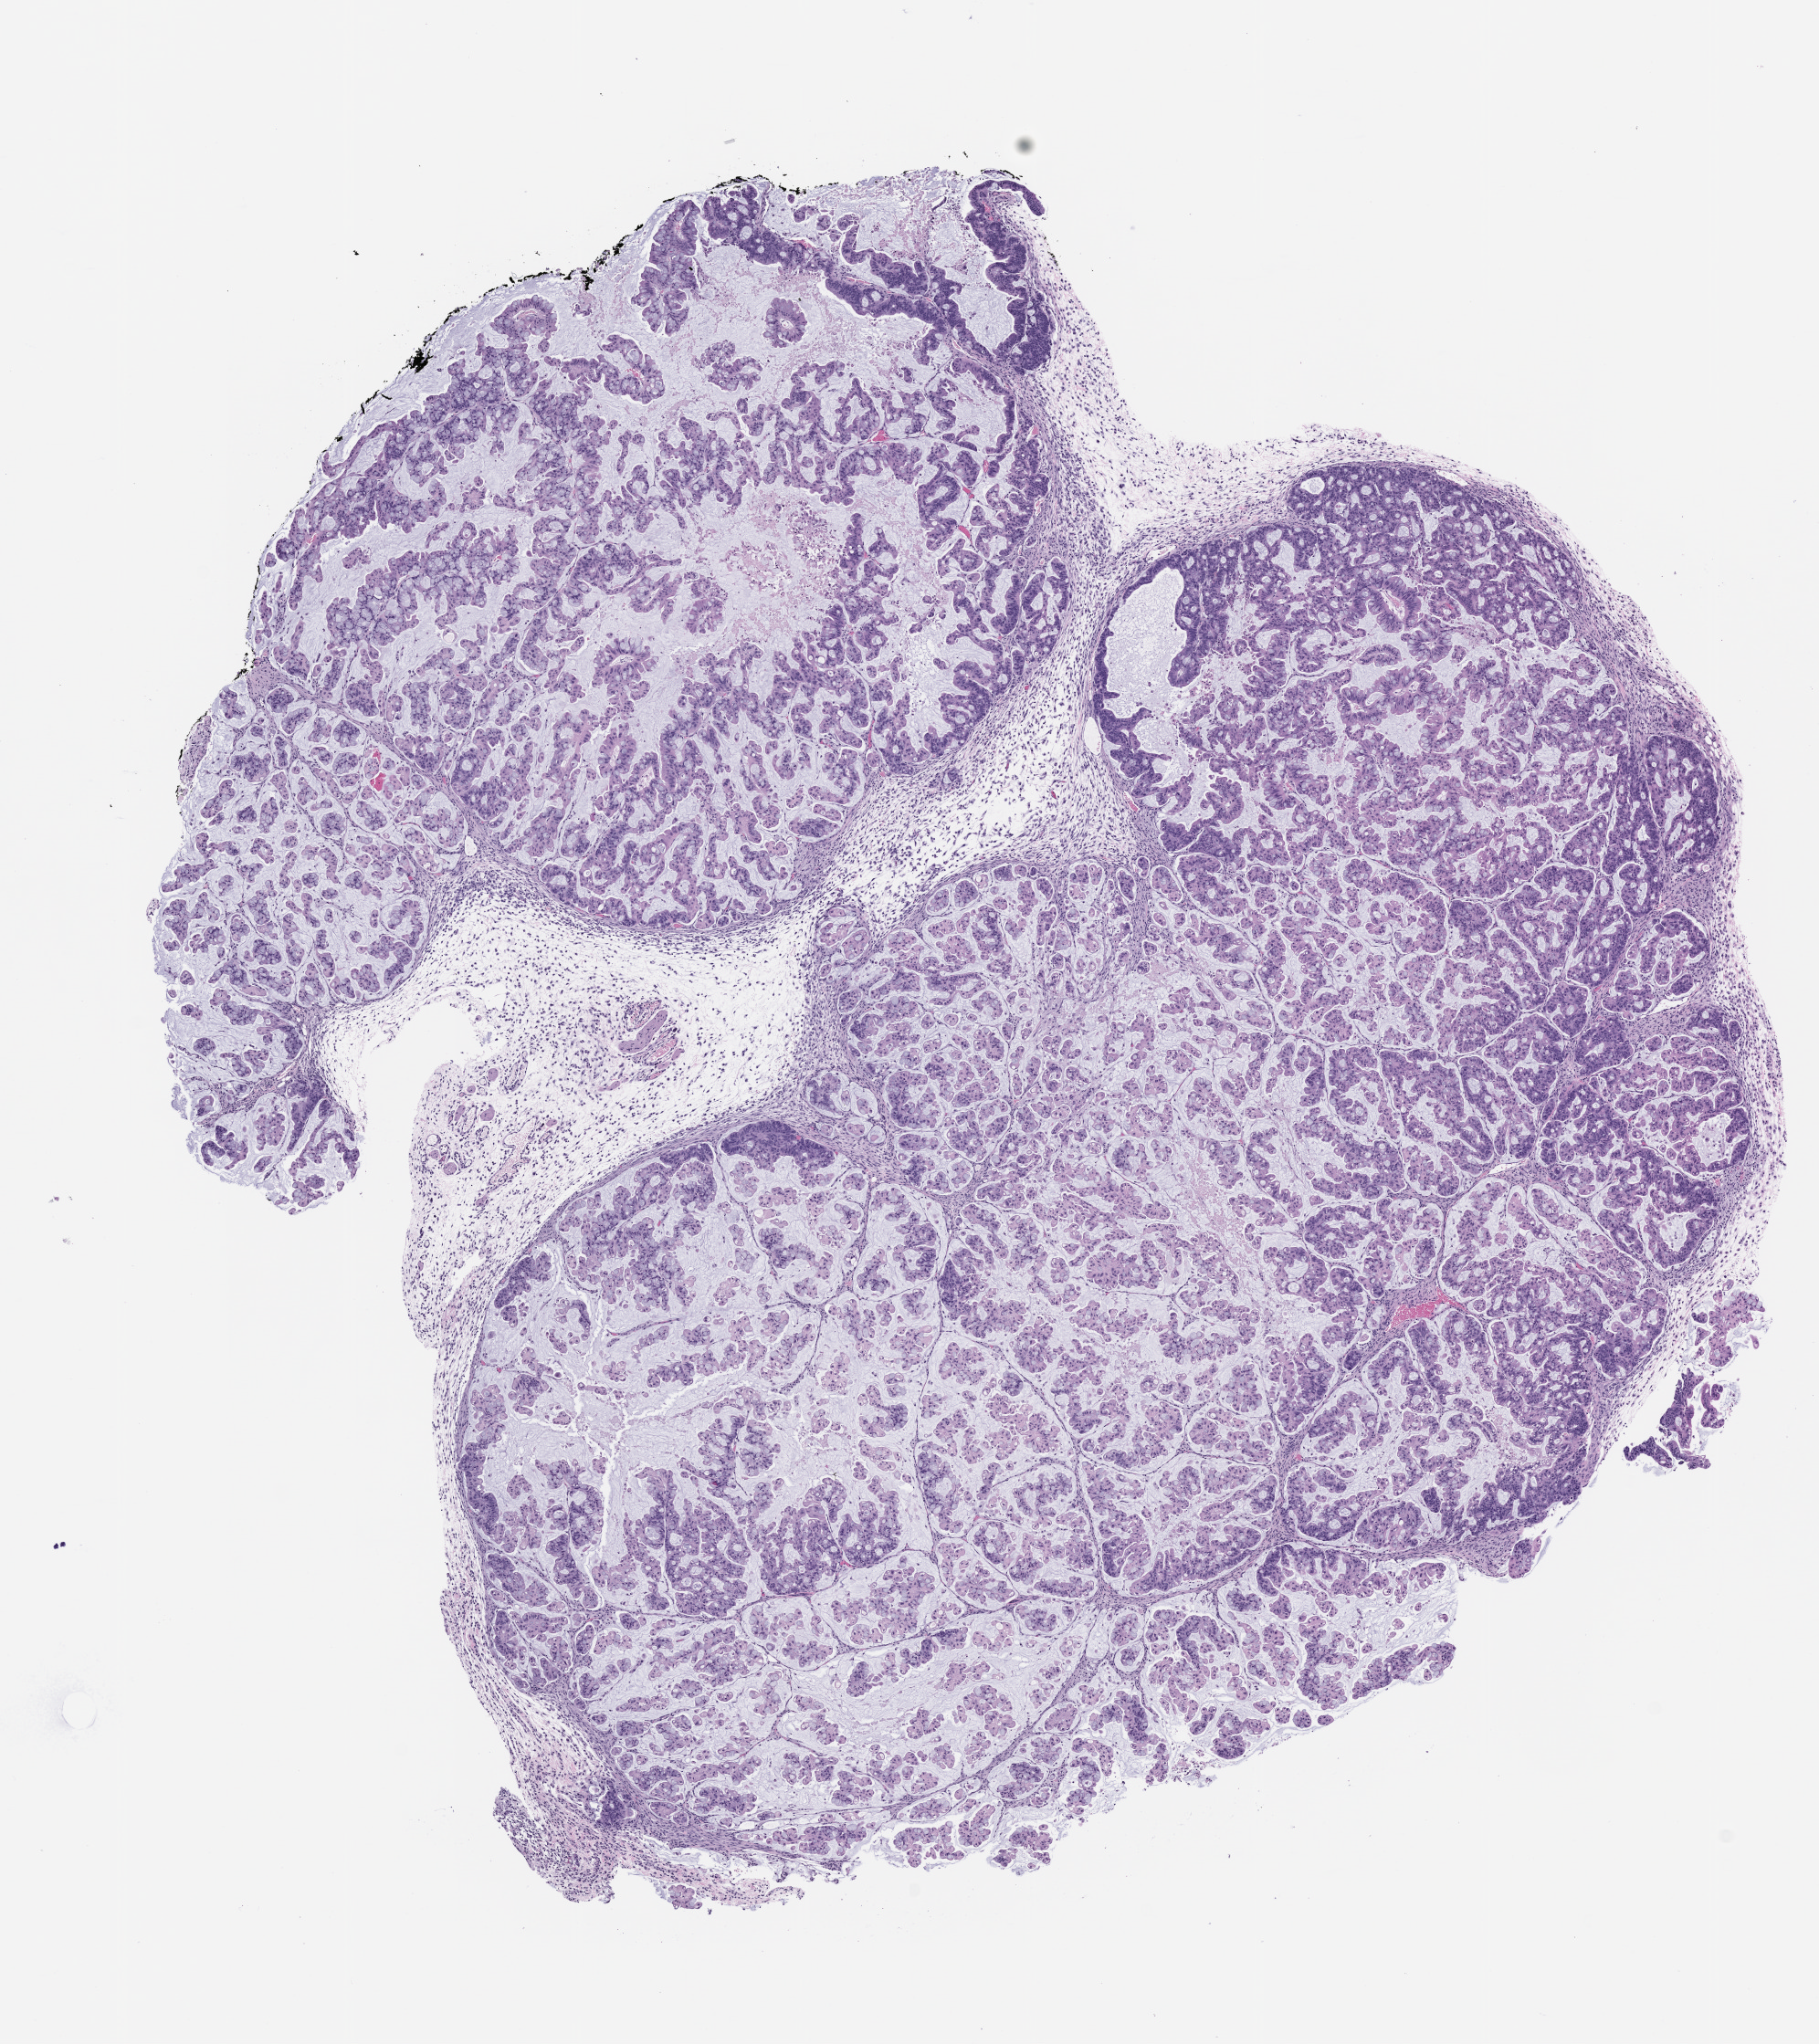
Whole-slide image, haematoxylin and eosin: patient-derived xenograft (human tumor grown in a mouse), passage 0, whole scanned area (about 8.0 x 9.0 mm) shown as a low-resolution overview, FFPE section, originating tumor site category: colon.
• originating patient diagnosis: Colon Adenocarcinoma